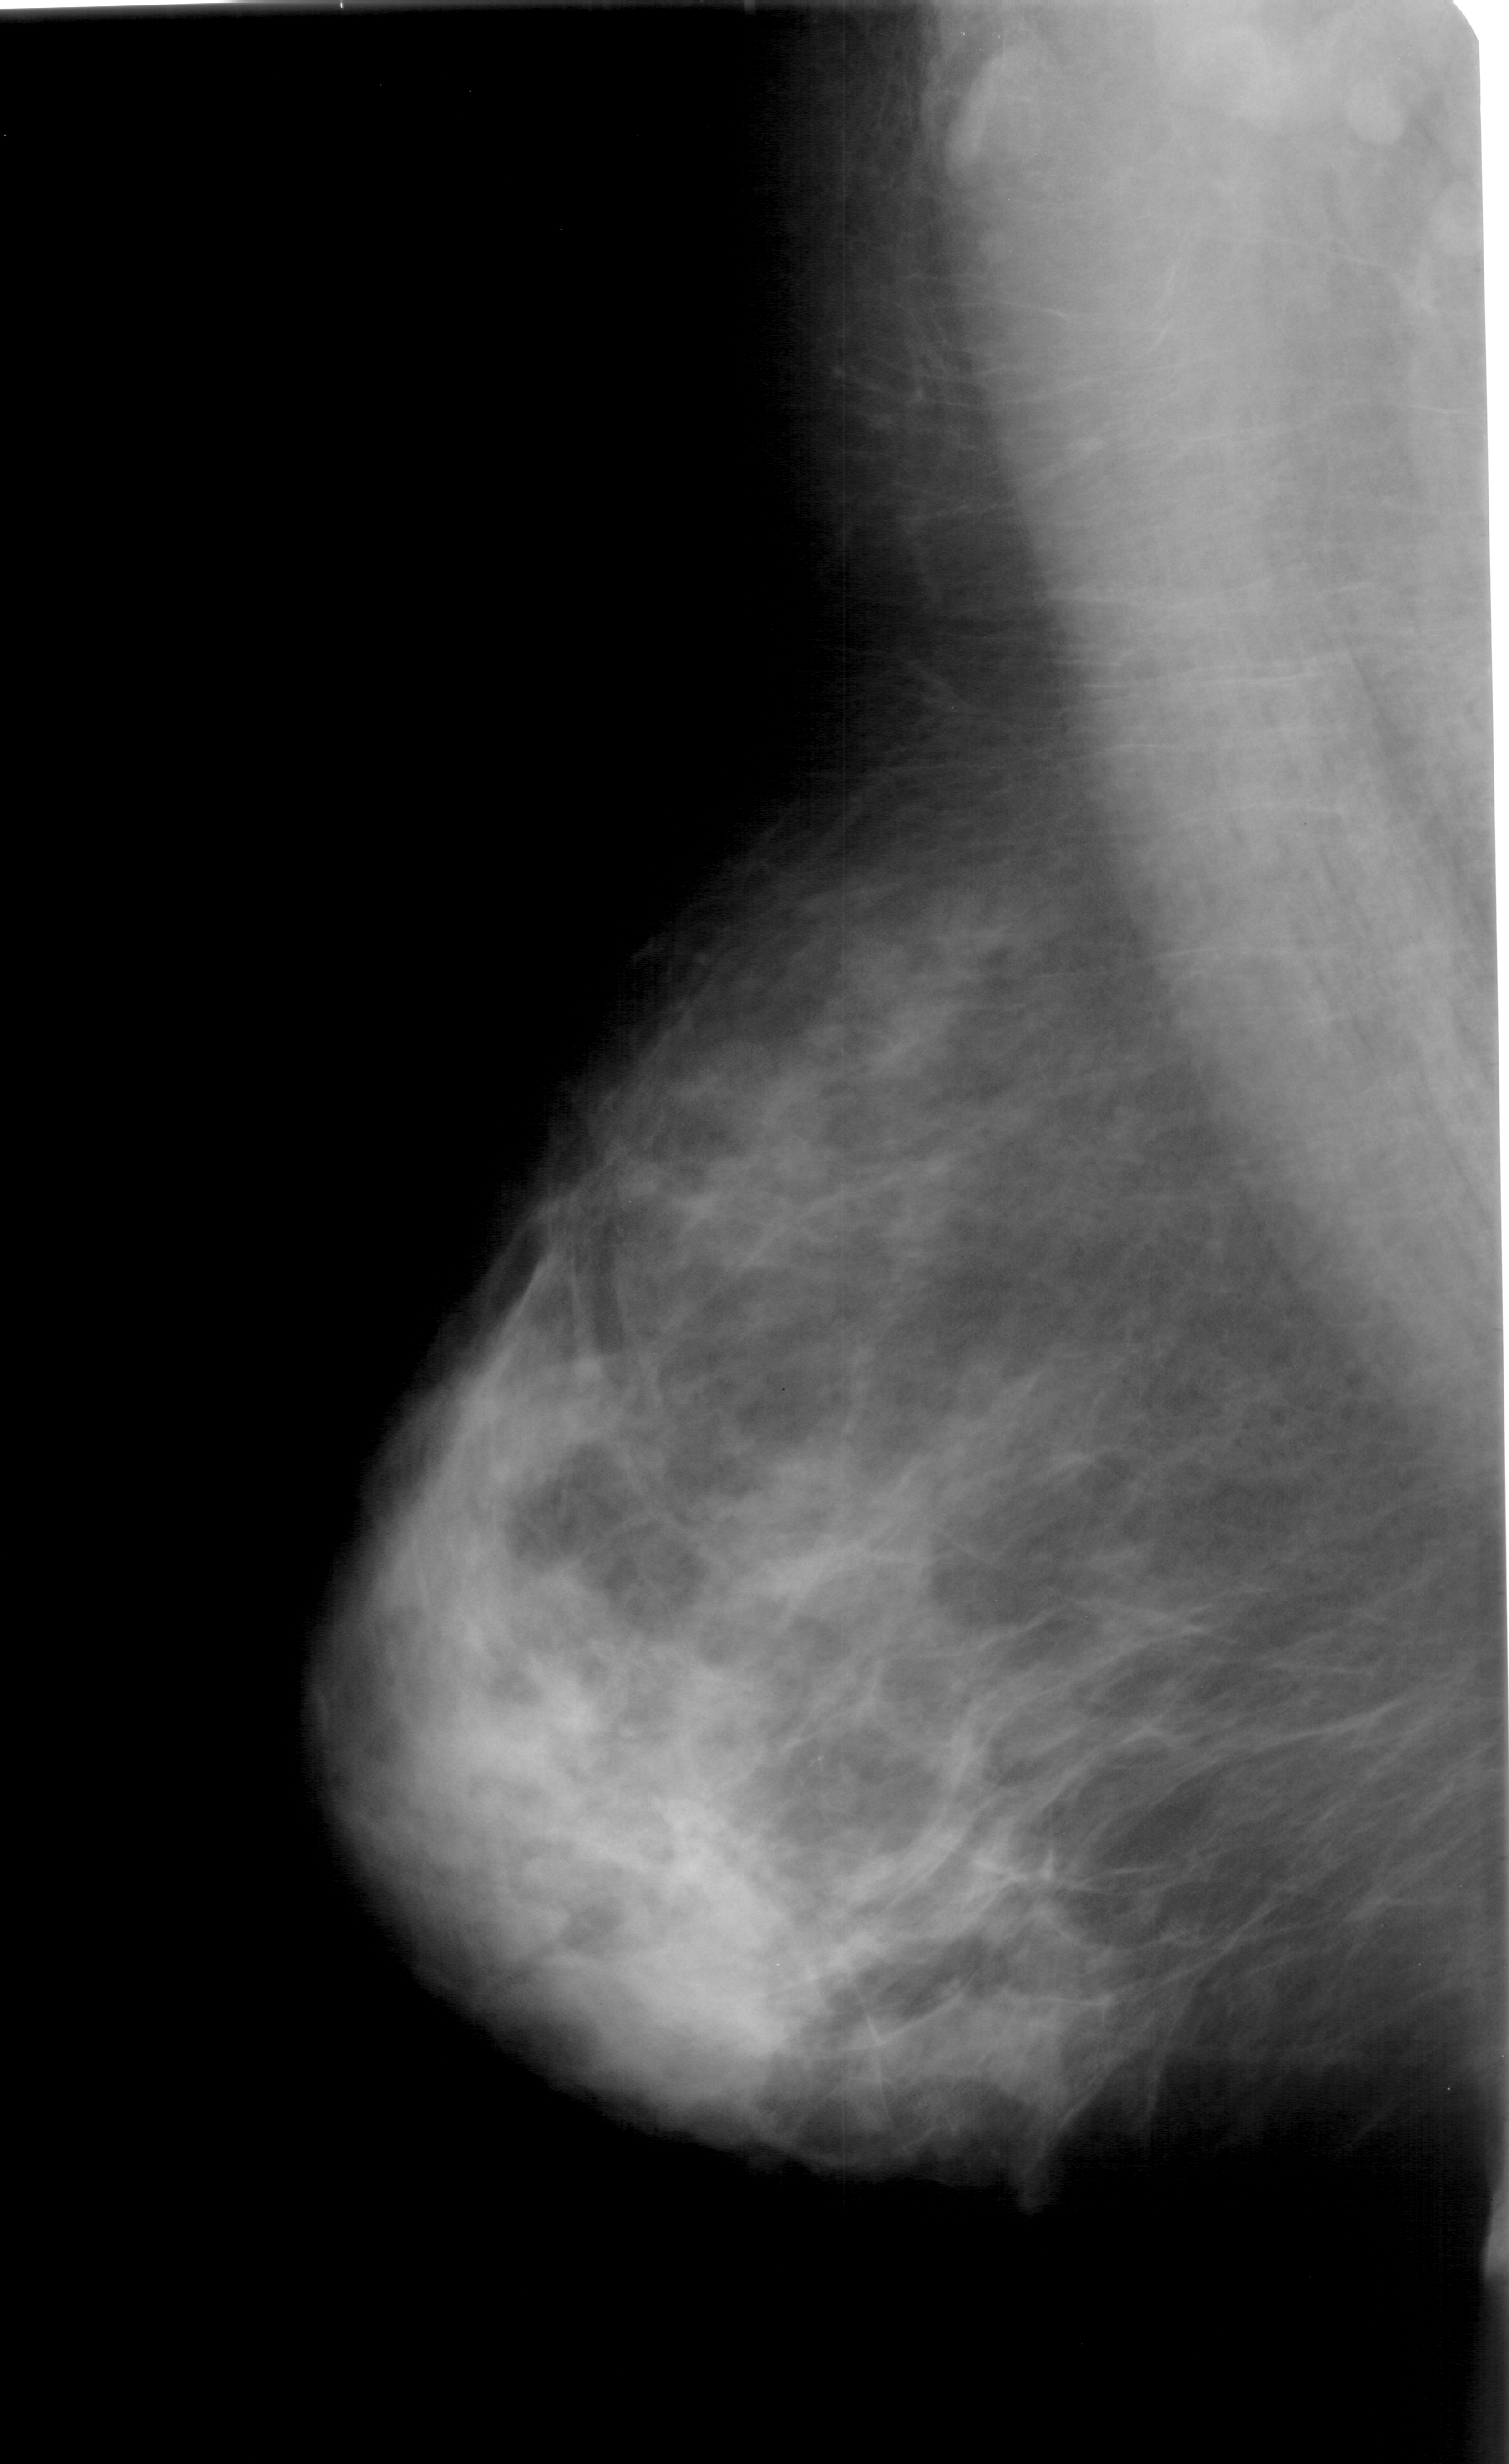
Mammogram (digitized film). Left breast. Mediolateral oblique (MLO) view. BI-RADS breast density category 4 (scale 1–4). 1509 × 2464 image matrix.
Marked abnormalities (boxes around the expert regions of interest):
- calcifications, morphology pleomorphic, distribution clustered; BI-RADS assessment category 4; subtlety rating 2 on a 1 (subtle) to 5 (obvious) scale; pathology (as recorded): benign: box from (x=810, y=1745) to (x=844, y=1775) px